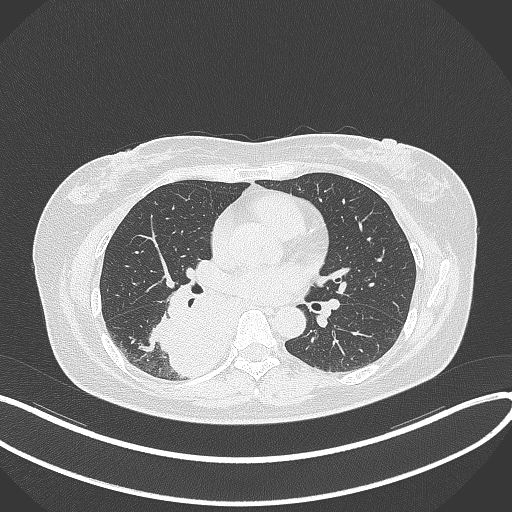
Chest CT, one axial slice; reconstruction kernel B70f; 120 kVp; lung window (W 1500 / L -600 HU); 1 mm slice thickness; 512 × 512 image matrix, field of view 400 × 400 mm. Patient: female, 54 years. From the clinical record (not read from this slice): clinical TNM (as recorded): T4 N0 M0.
Outlined on this slice (rectangle marked by the reading radiologist):
- lung tumour (recorded histology: adenocarcinoma): bounding box (x1, y1, x2, y2) in pixels: (155, 281, 238, 382)